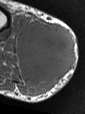
MRI of an extremity soft-tissue mass, one axial slice; position 22 of 47 along the scan axis; MR volume resampled by the dataset authors to the PET/CT grid (not the native acquisition matrix); 85 × 114 image matrix, field of view 83 × 111 mm. Male patient. Case-level facts recorded for this patient, not image findings: histological type: pleiomorphic liposarcoma; grade: high; site of the primary tumour: right calf.
Annotated regions visible in this slice (expert contour drawn on MRI and transferred to this co-registered scan by the dataset authors):
- gross tumour volume including surrounding oedema: bounding box (x1, y1, x2, y2) in pixels: (17, 16, 75, 95)
- gross tumour volume (mass): (17, 23, 75, 81)